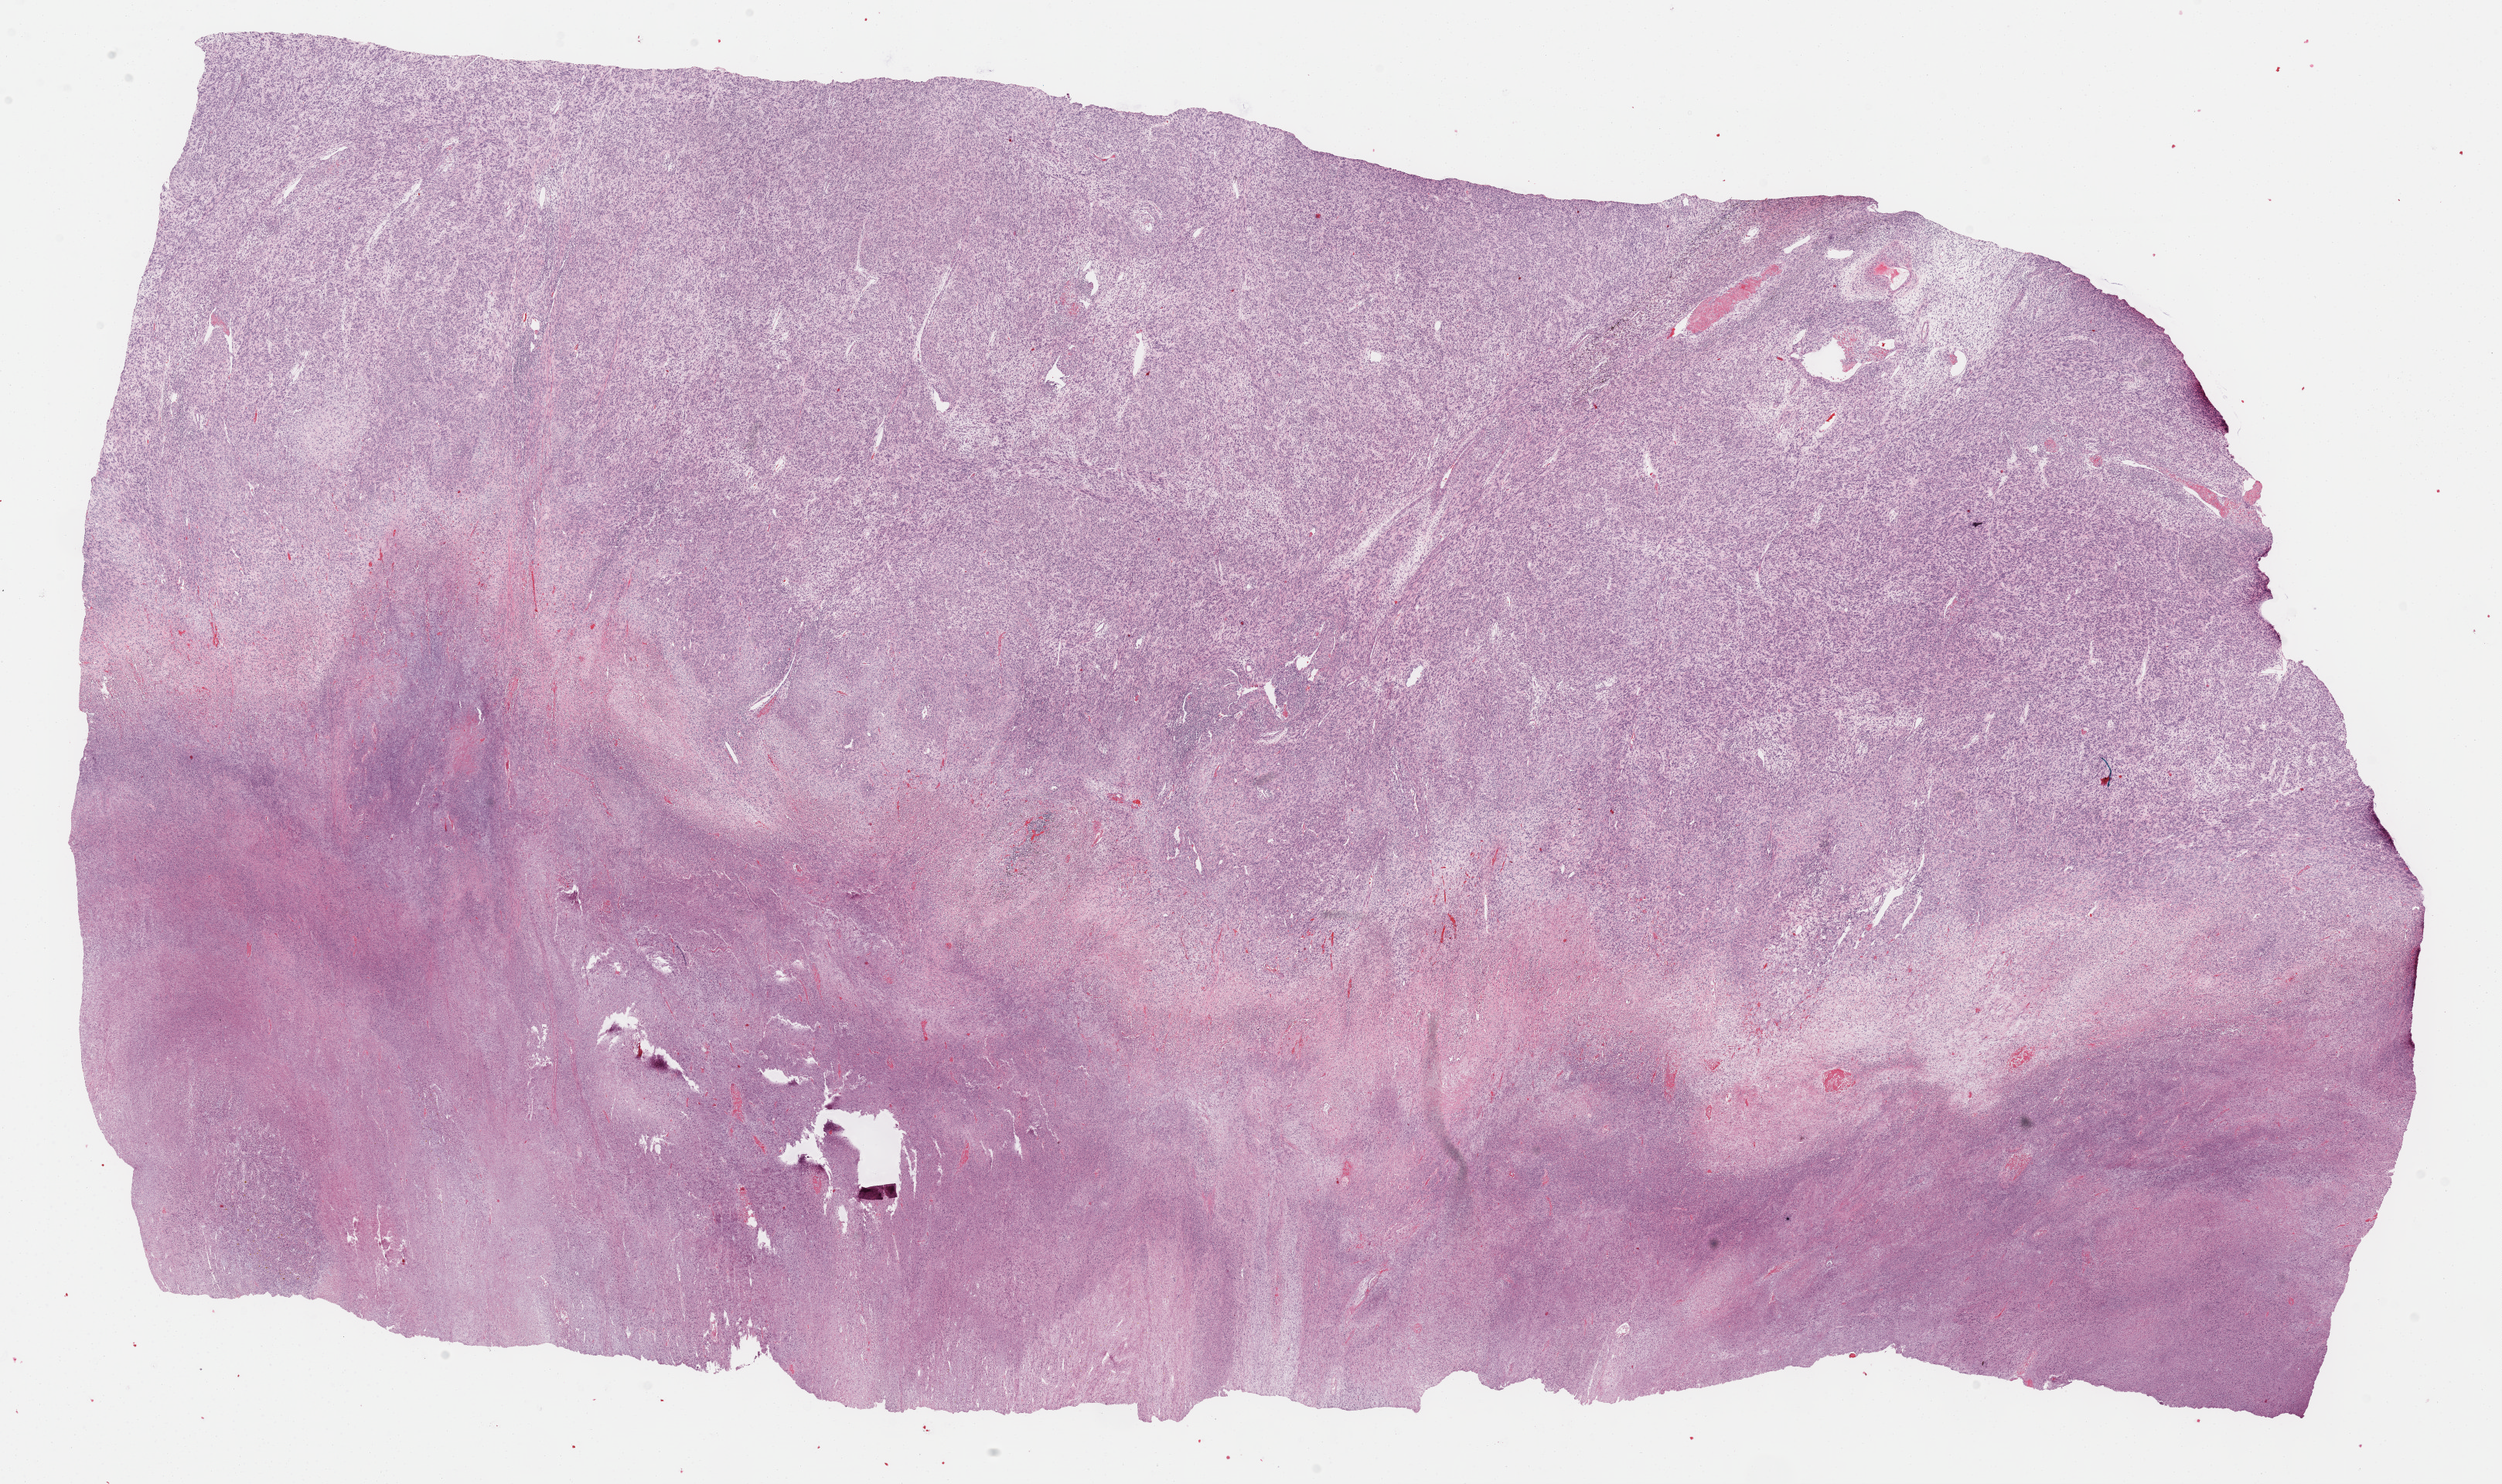
Digitized H&E-stained tissue section (whole slide), a low-resolution overview of the entire scanned area, about 26.2 x 15.5 mm; formalin-fixed paraffin-embedded (FFPE) diagnostic section; retroperitoneum and peritoneum, primary tumour sample. Male, age 52 years at initial diagnosis.
Pathologic diagnosis: Undifferentiated sarcoma (retroperitoneum).